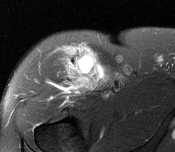
MRI of an extremity soft-tissue mass, one axial slice; position 110 of 116 along the scan axis; T2-weighted fat-saturated; MR volume resampled by the dataset authors to the PET/CT grid (not the native acquisition matrix); 175 × 152 image matrix. Male patient. From the clinical record (not read from this slice): histological type: pleiomorphic leiomyosarcoma; grade: intermediate; site of the primary tumour: right thigh.
Outlined on this slice (expert contour drawn on MRI and transferred to this co-registered scan by the dataset authors):
- gross tumour volume including surrounding oedema: bounding box [x1, y1, x2, y2] px = [65, 49, 105, 93]
- gross tumour volume (mass): [72, 58, 103, 89]